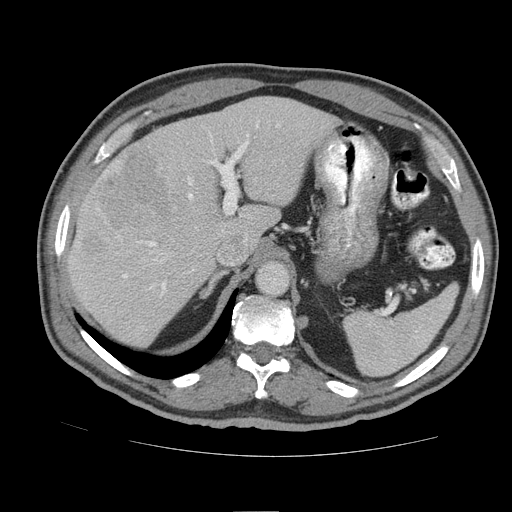
Contrast-enhanced abdominal CT (liver protocol), one axial slice. Slice 61 of 105 in the series (ordered by position). Reconstruction kernel STANDARD. 140 kVp. Soft-tissue window (W 400 / L 40 HU). 512 × 512 image matrix, field of view 380 × 380 mm. From the clinical record (not read from this slice): diagnosis: hepatocellular carcinoma (patient treated with transarterial chemoembolisation; whether this scan precedes or follows treatment is not stated here); TNM stage (as recorded): Stage-IIIB; Child-Pugh class: A; tumour nodularity: multinodular.
Annotated regions visible in this slice (semi-automatically segmented with operator editing):
- liver parenchyma outside the tumour (the mass and vessels are separate outlines, so this box may not span the whole liver): bounding box <68,96,336,346> (left, top, right, bottom; pixels)
- mass: <81,144,179,257>
- liver vessels: <122,124,279,294>